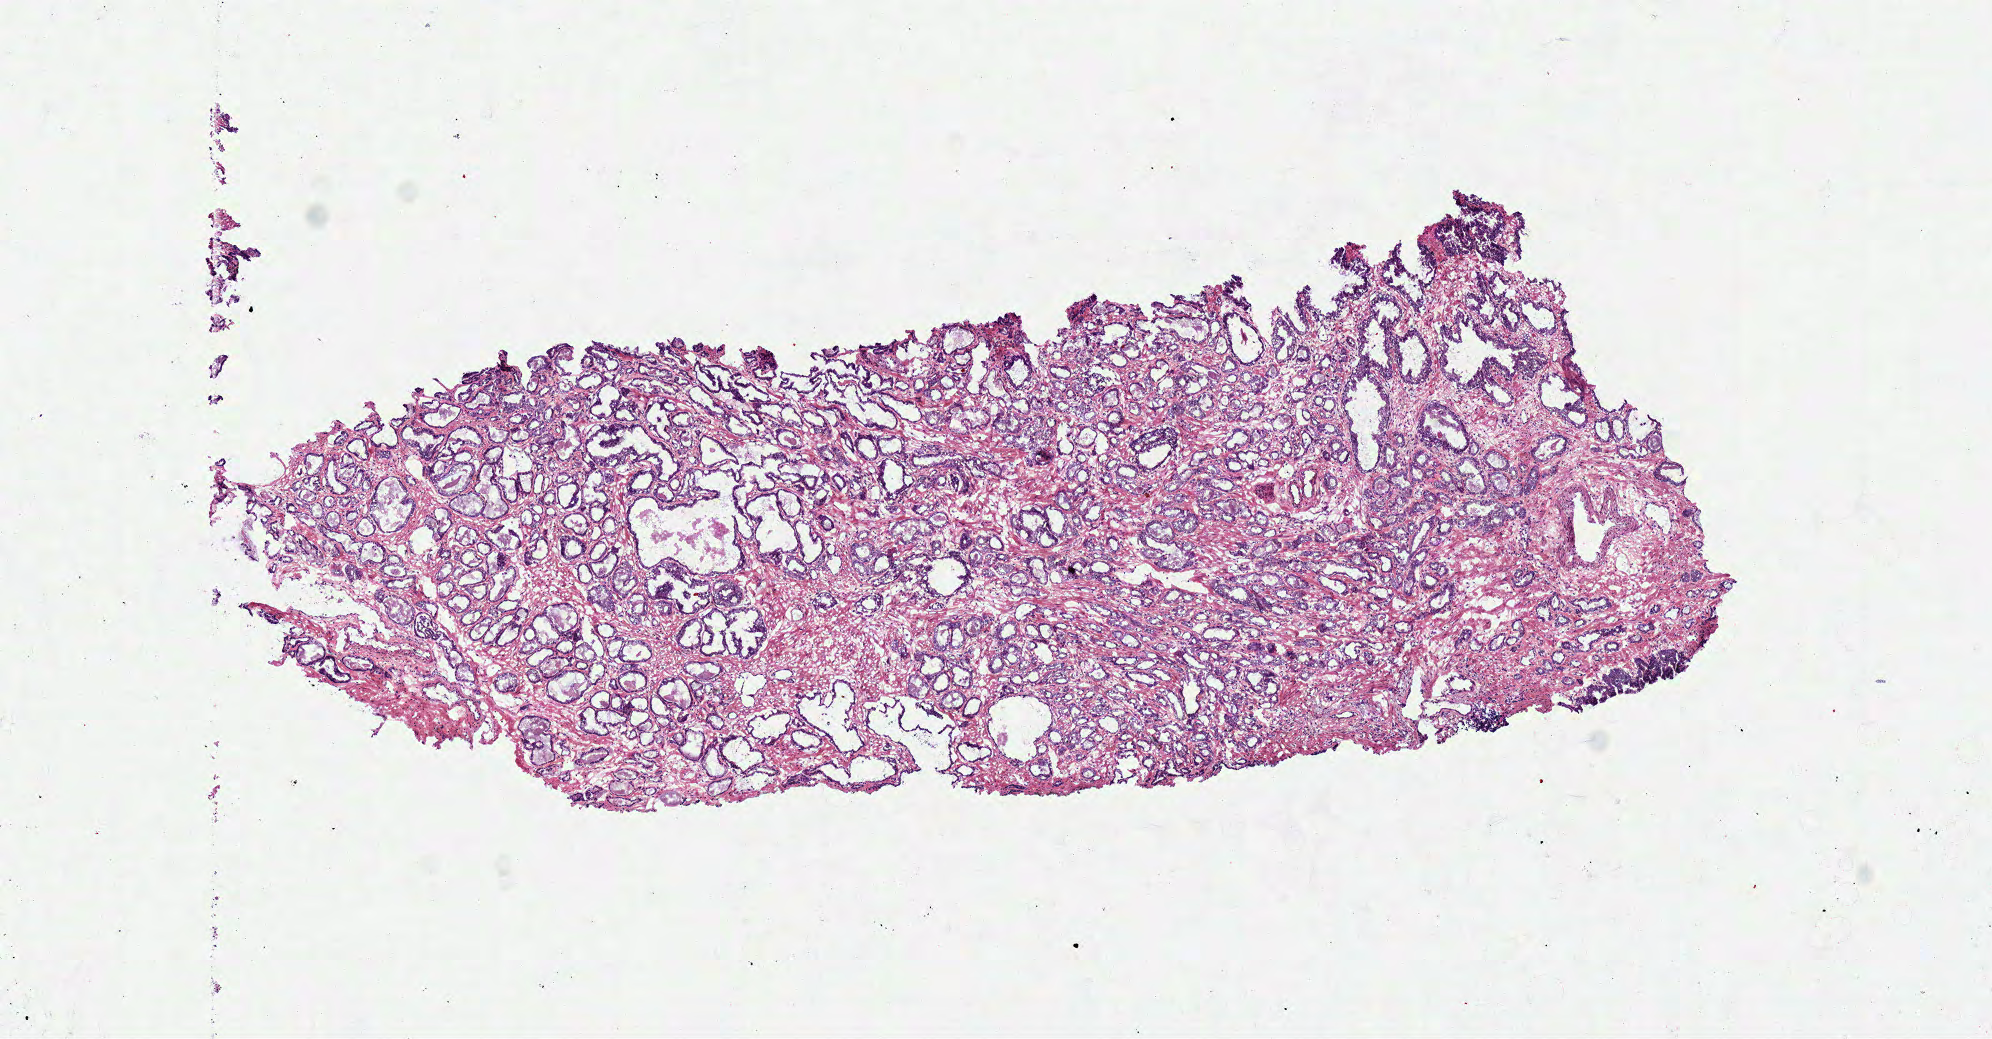
Digitized Hematoxylin and eosin (H&E) stained tissue section (whole slide) — low-resolution overview of the scanned area, about 7.8 x 4.1 mm (from a 40x scan). Frozen section. Prostate, primary tumour sample. Male, age 58 years at initial diagnosis. Gleason score: 7 (3+4). Slide review estimates, as recorded: tumour cells 60%, tumour nuclei 65%, normal cells 20%, stromal cells 20%, necrosis 0%. Inflammatory infiltration, as recorded: lymphocyte infiltration 2%, monocyte infiltration 0%, neutrophil infiltration 0%.
- histologic diagnosis: Acinar cell carcinoma
- laterality: bilateral